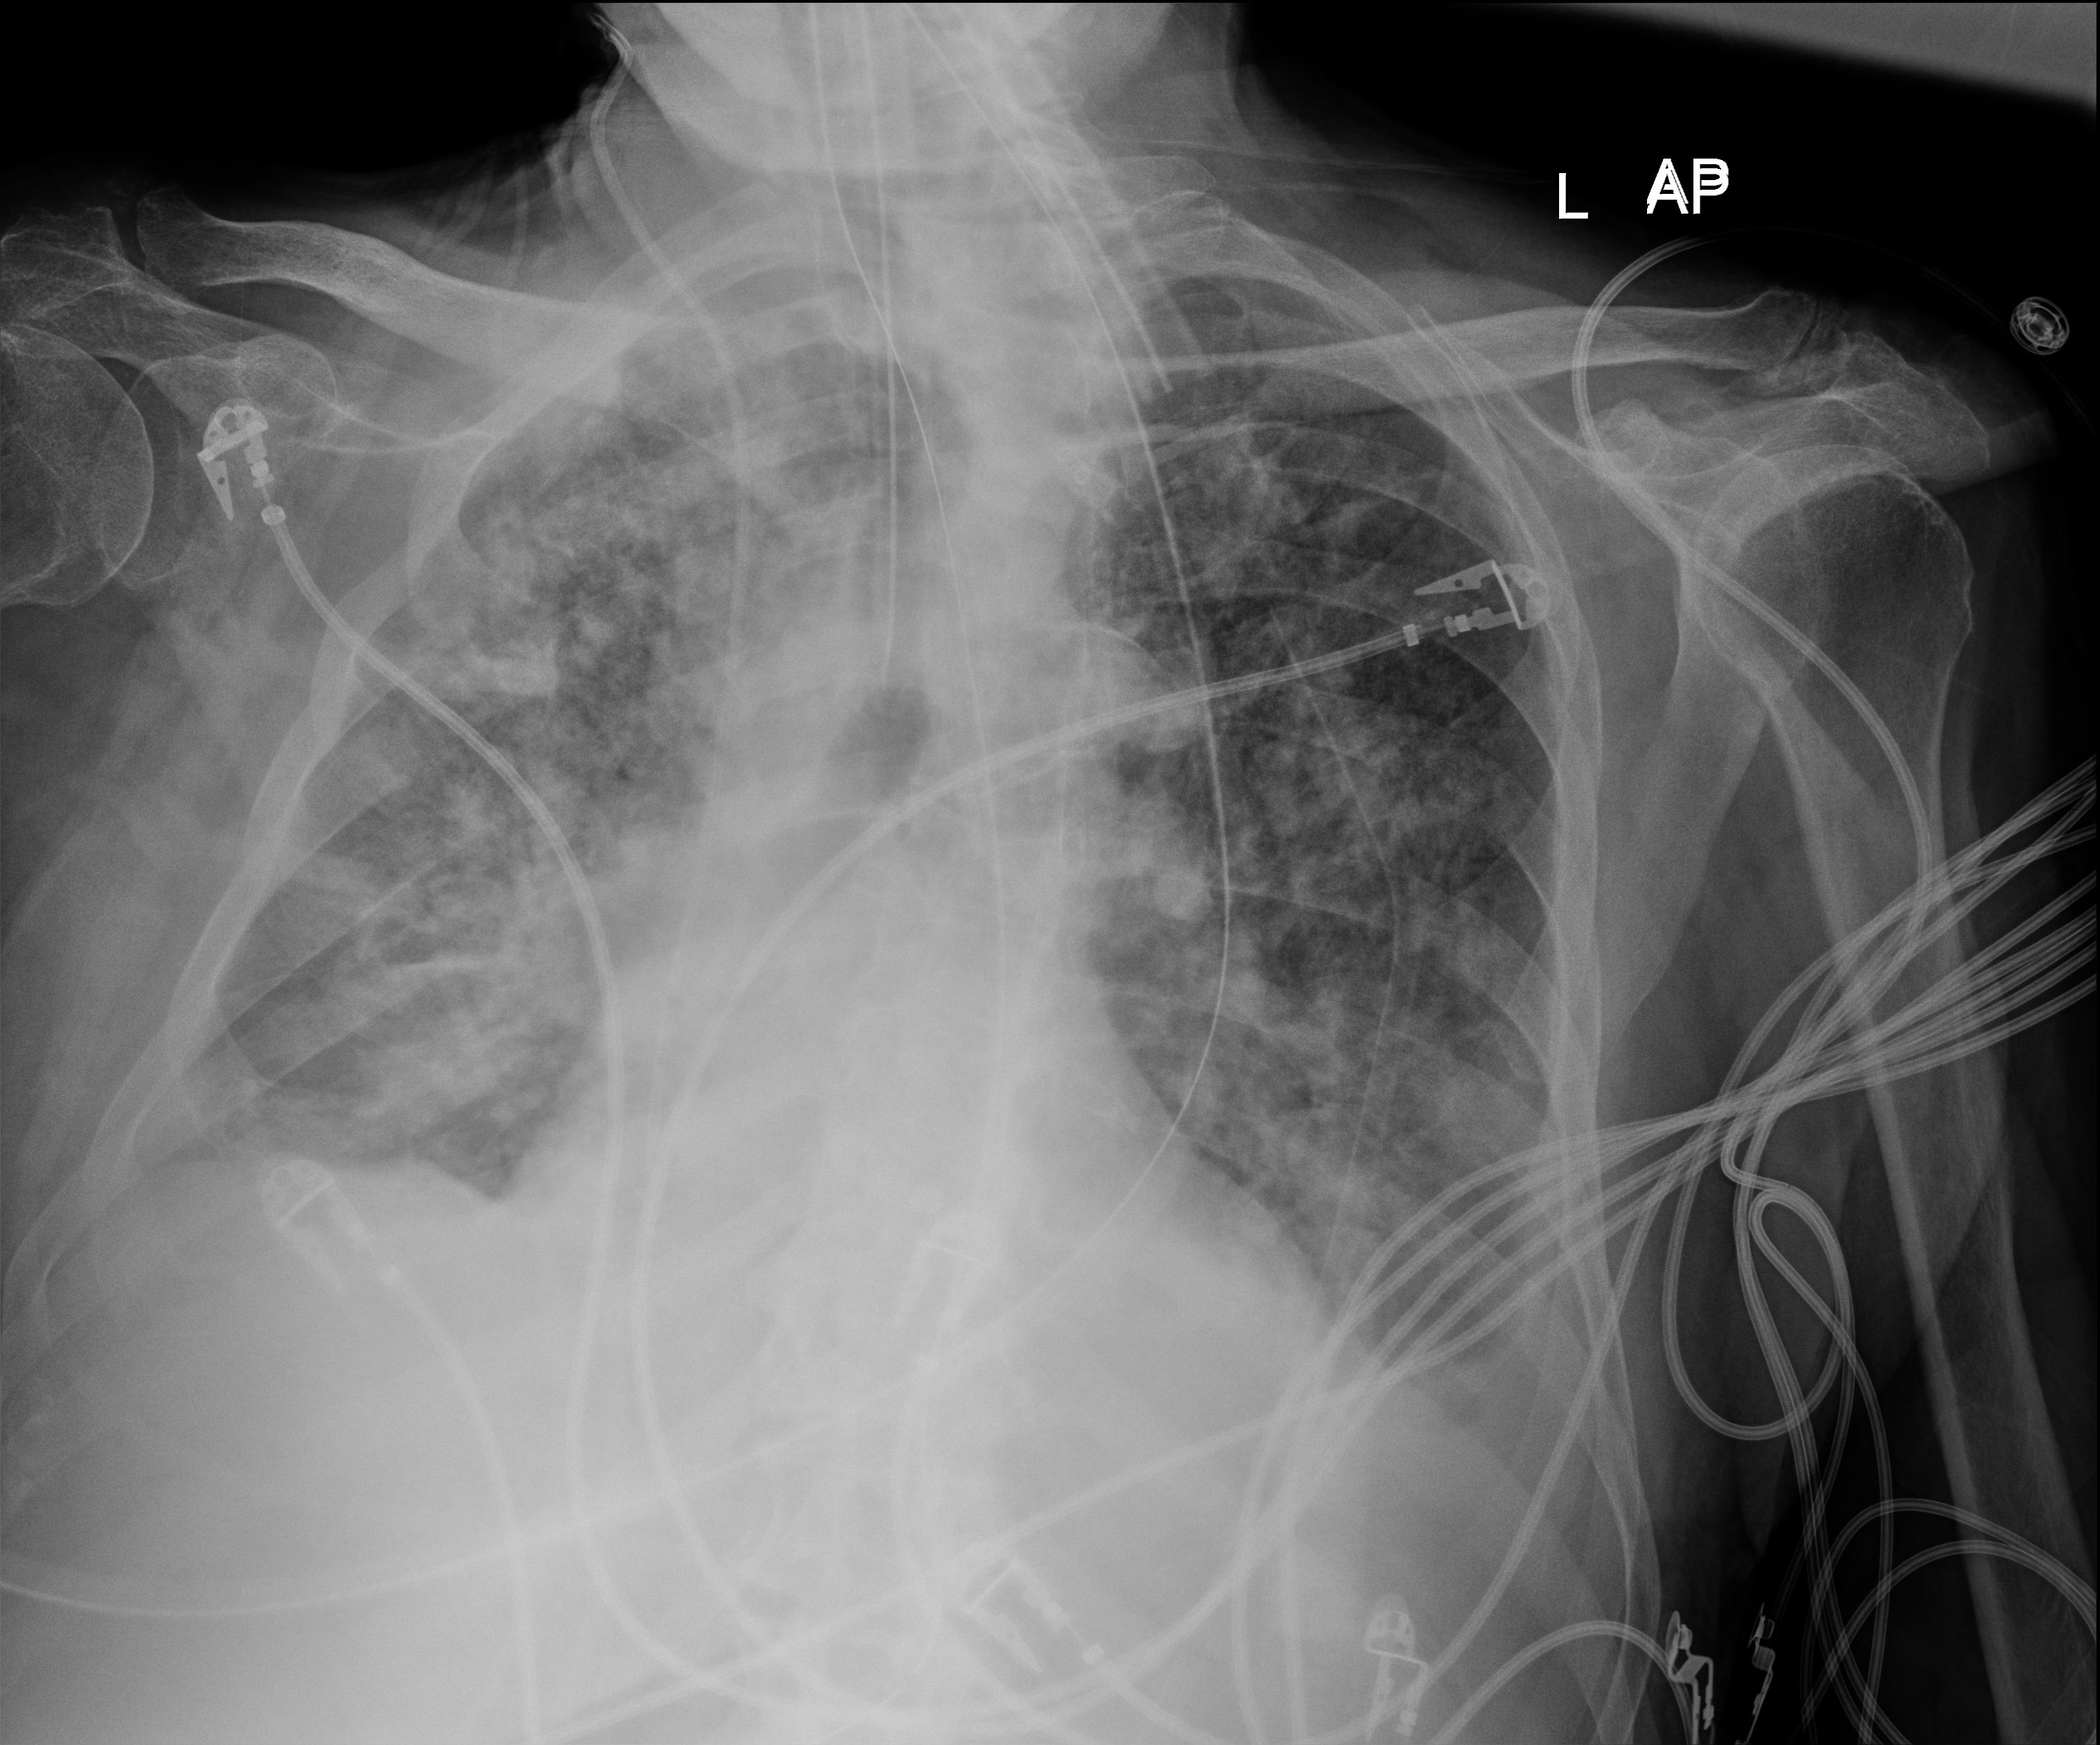
Chest X-ray (portable); anteroposterior (AP) projection. Patient hospitalised with COVID-19; male, aged 75–90 years.
From the hospital-stay record, not from the radiograph (when in the stay this image was taken is not recorded):
- mechanically ventilated during this hospital stay: yes
- admitted to intensive care during this hospital stay: yes
- COPD (admission record): no